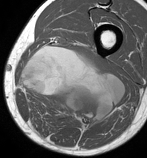
MRI of an extremity soft-tissue mass, one axial slice. MR volume resampled by the dataset authors to the PET/CT grid (not the native acquisition matrix). 3.27 mm slice thickness. 147 × 158 image matrix. Male patient. From the clinical record (not read from this slice): histological type: undifferentiated pleomorphic liposarcoma; grade: high; site of the primary tumour: left thigh.
Structures marked on this image (expert contour drawn on MRI and transferred to this co-registered scan by the dataset authors):
- gross tumour volume including surrounding oedema: bounding box <19,46,125,128> (left, top, right, bottom; pixels)
- gross tumour volume (mass): <21,46,125,128>